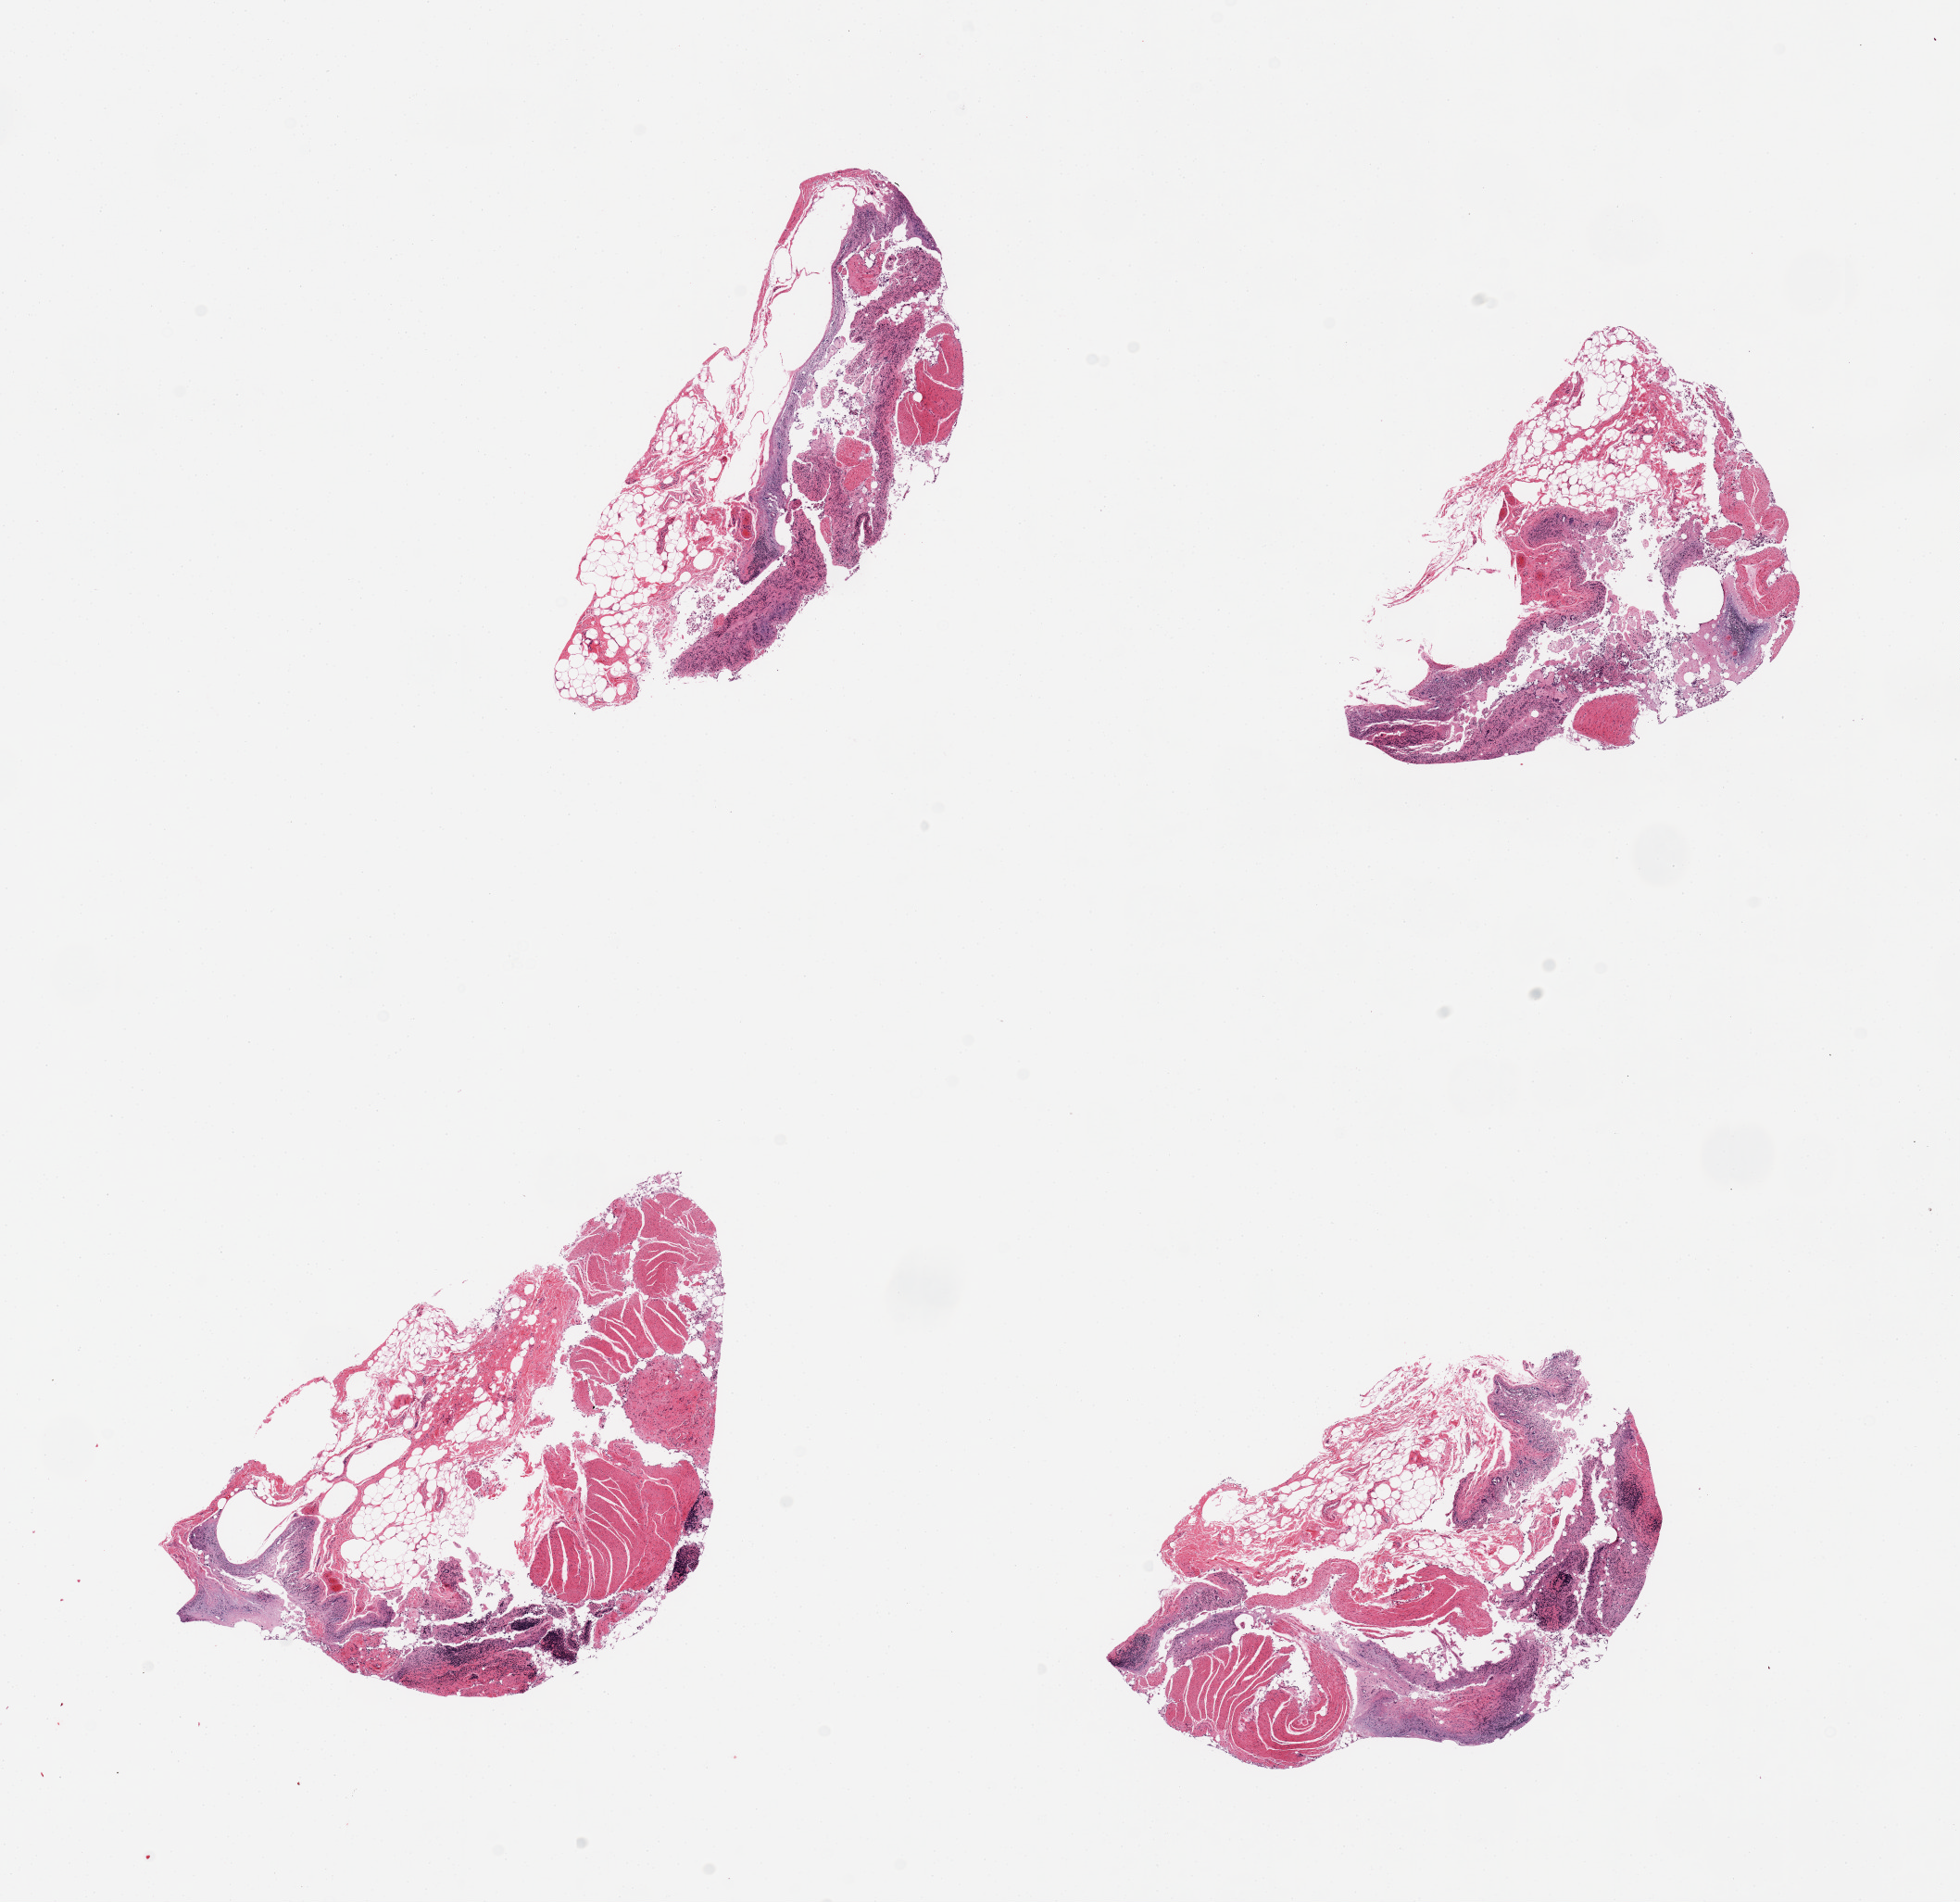
Digitized hematoxylin and eosin (H&E)-stained section — shown as a low-resolution overview of the whole scanned area (about 16.7 x 16.2 mm, acquisition: 20x scan), PAXgene-fixed paraffin-embedded (PFPE) section, target tissue: ileum, donor tissue sample. Donor: male.
- reviewer comment on this tissue sample: 4 pieces, mucosa totally autolyzed, lymphoid elements are 10-15% of specimen; aggregates